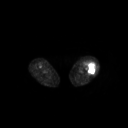
FDG PET of an extremity soft-tissue mass (from a PET/CT study), one axial slice. Position 202 of 267 along the scan axis. 128 × 128 image matrix. Female patient, age 62 years. Case-level facts recorded for this patient, not image findings: histological type: undifferentiated – high grade; grade: high; site of the primary tumour: left thigh.
Structures marked on this image (expert contour drawn on MRI and transferred to this co-registered scan by the dataset authors):
- gross tumour volume including surrounding oedema: bounding box <84,61,96,74> (left, top, right, bottom; pixels)
- gross tumour volume (mass): <92,64,93,65>